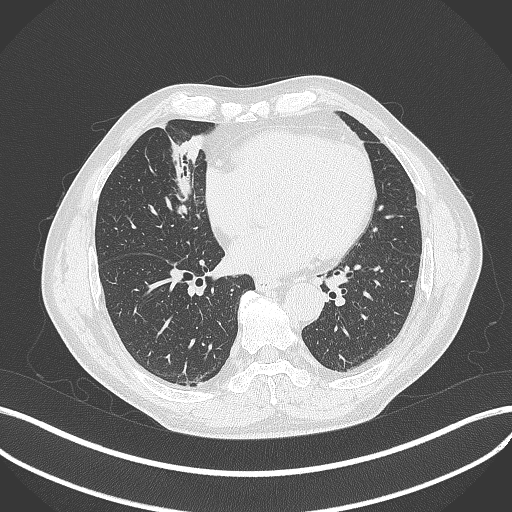
Chest CT, one axial slice; position 160 of 429 along the scan axis; lung window (W 1500 / L -600 HU); 512 × 512 image matrix, field of view 400 × 400 mm. Patient: male, 61 years. From the clinical record (not read from this slice): clinical TNM (as recorded): T2b N1 M0.
Outlined on this slice (rectangle marked by the reading radiologist):
- lung tumour (recorded histology: squamous cell carcinoma): bounding box [x1, y1, x2, y2] px = [167, 161, 200, 211]